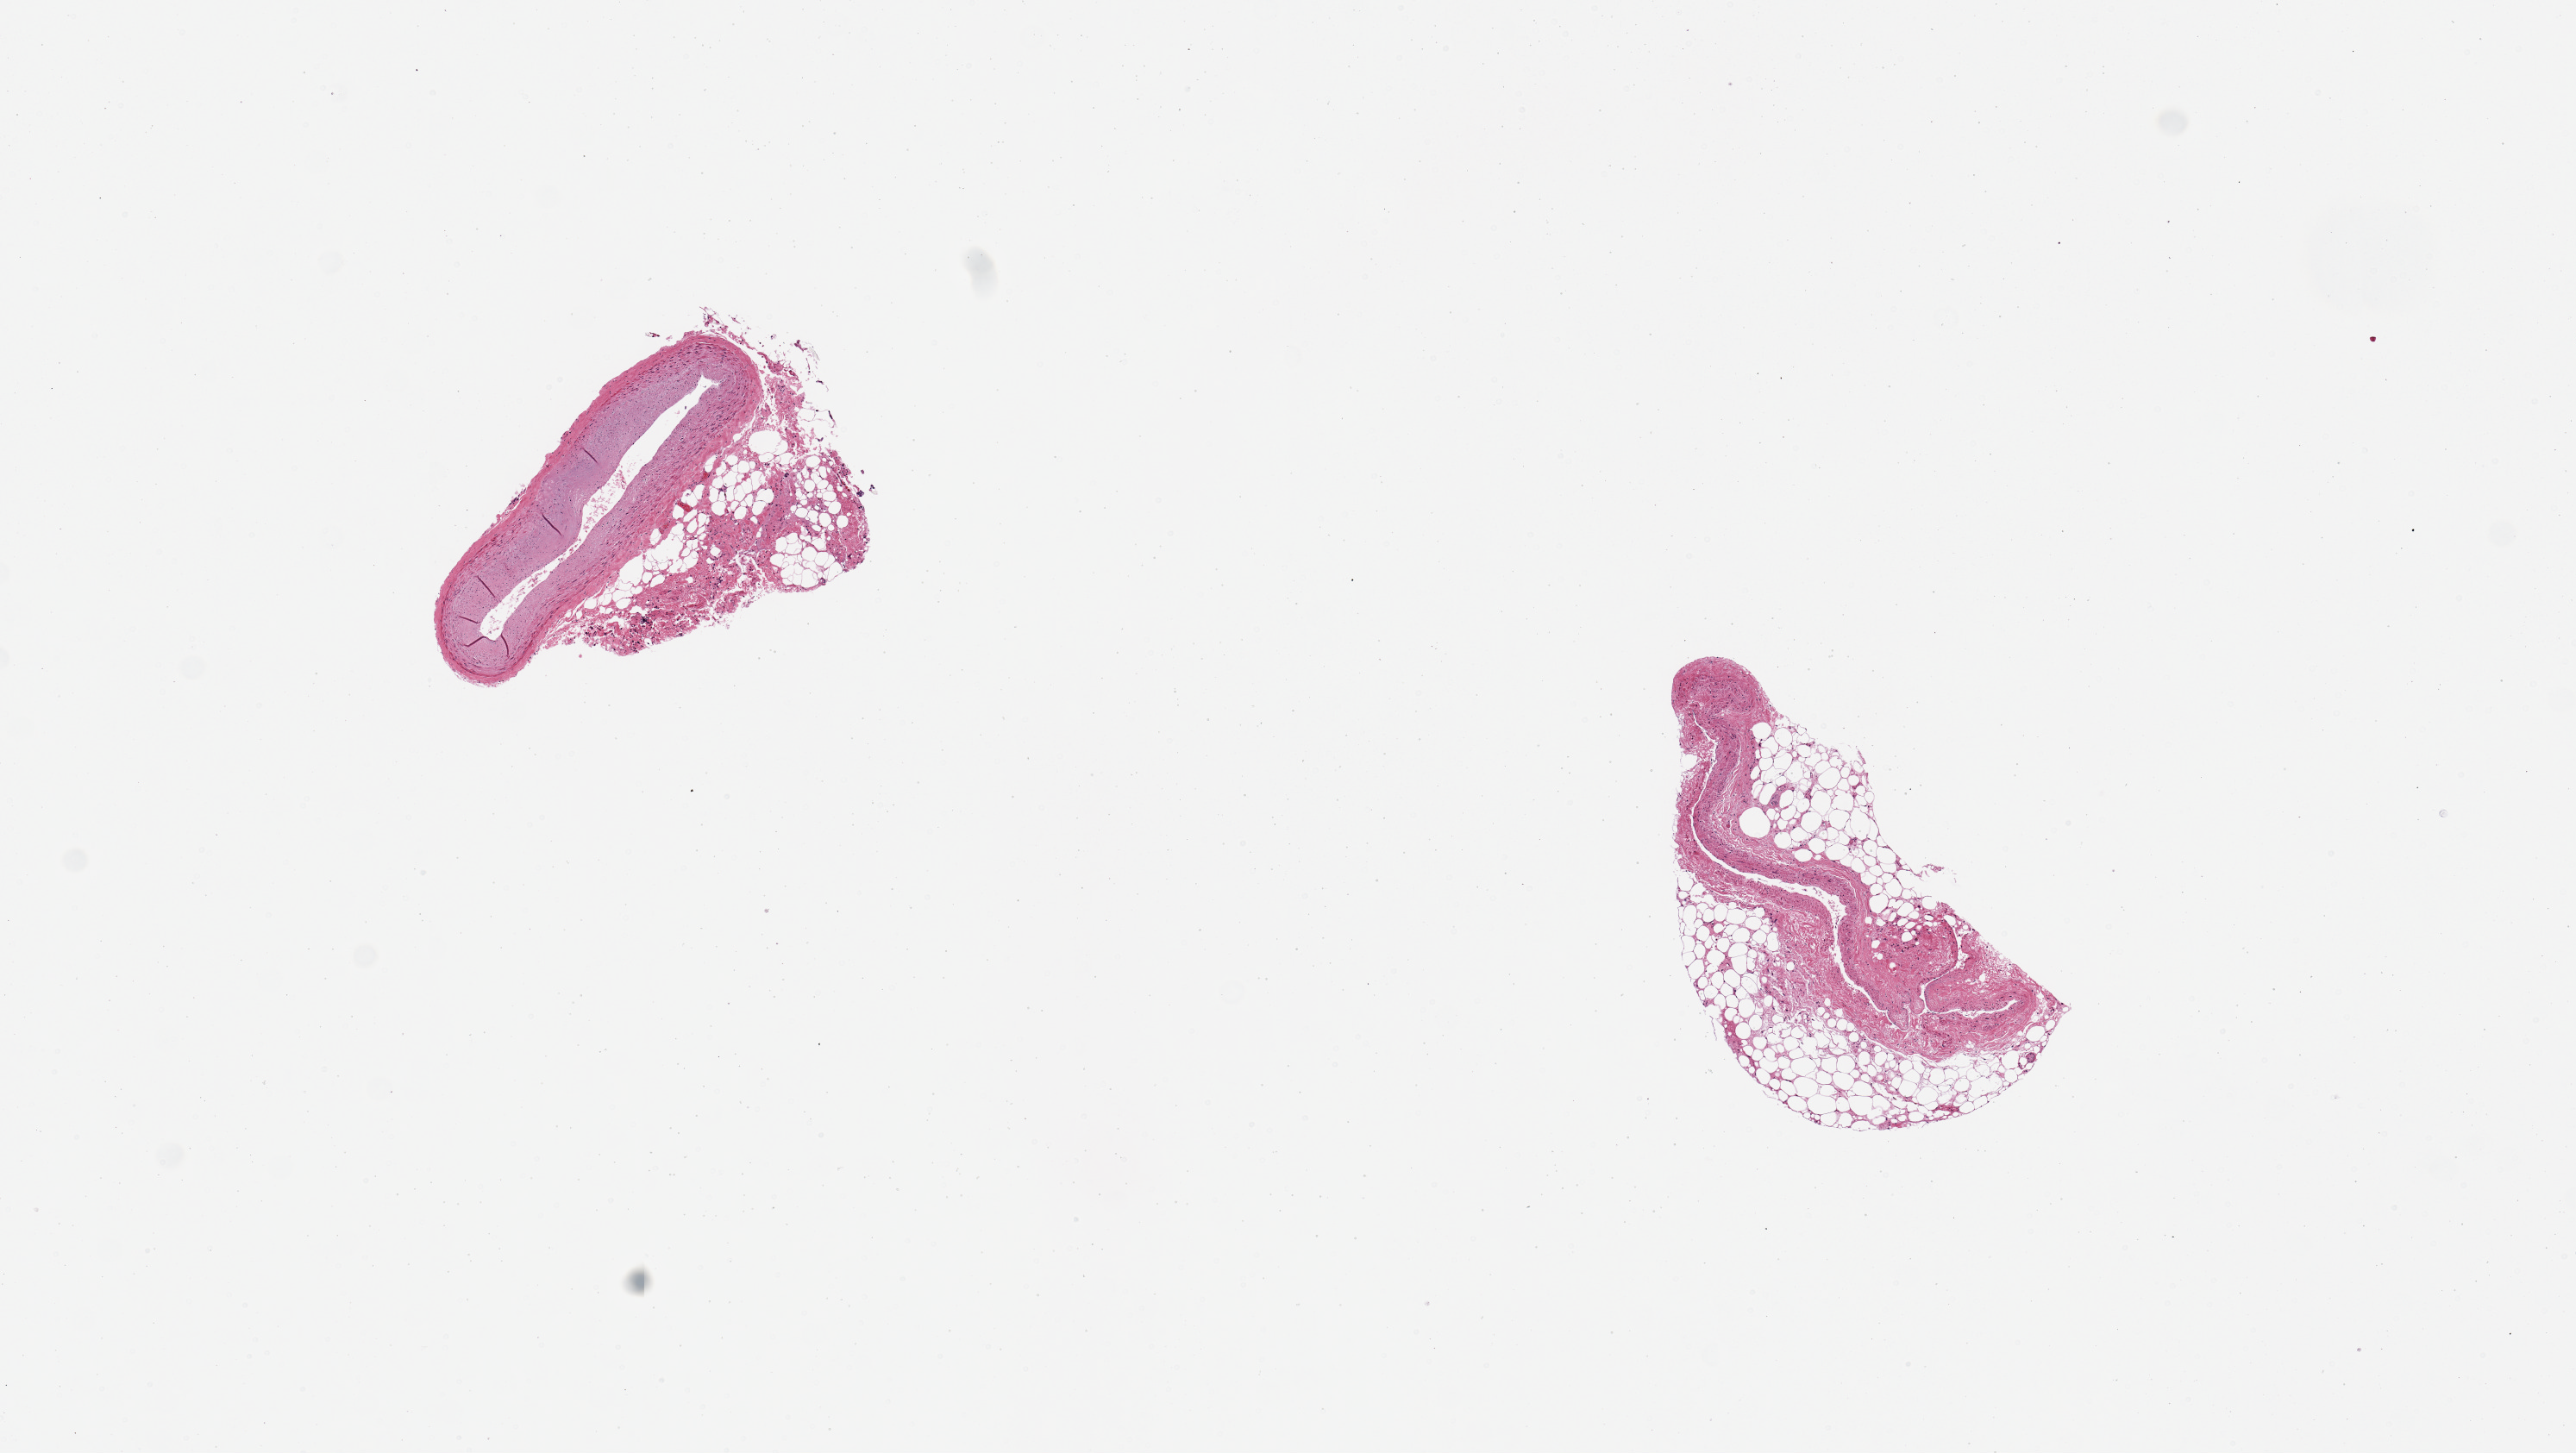
Hematoxylin and eosin (H&E) whole-slide image, whole scanned area (about 11.8 x 6.7 mm, from a 20x scan) shown as a low-resolution overview. PAXgene-fixed, paraffin-embedded tissue. Target tissue: coronary artery. Tissue donor sample. Donor: female.
* review note (as recorded): 2 pieces; 1 artery, 1 vein; 50% external fat